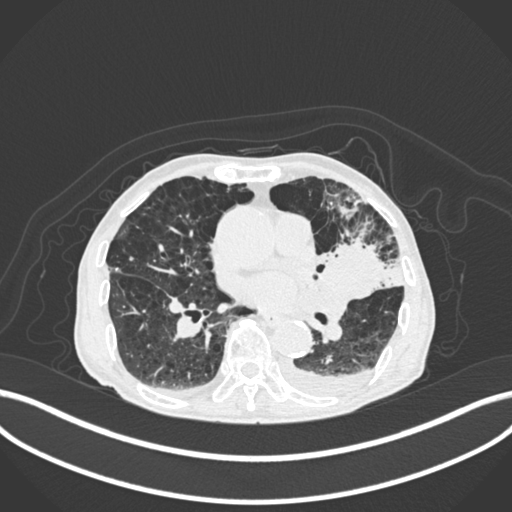
Chest CT, one axial slice; slice 101 of 400 in the series (ordered by position); lung window (W 1500 / L -600 HU); 1 mm slice thickness; 512 × 512 image matrix, field of view 400 × 400 mm. Patient: male, 90 years or older. From the clinical record (not read from this slice): clinical TNM (as recorded): T2b N1 M0.
Outlined on this slice (bounding box drawn by a radiologist):
- lung tumour (recorded histology: squamous cell carcinoma): bounding box <315,230,388,303> (left, top, right, bottom; pixels)